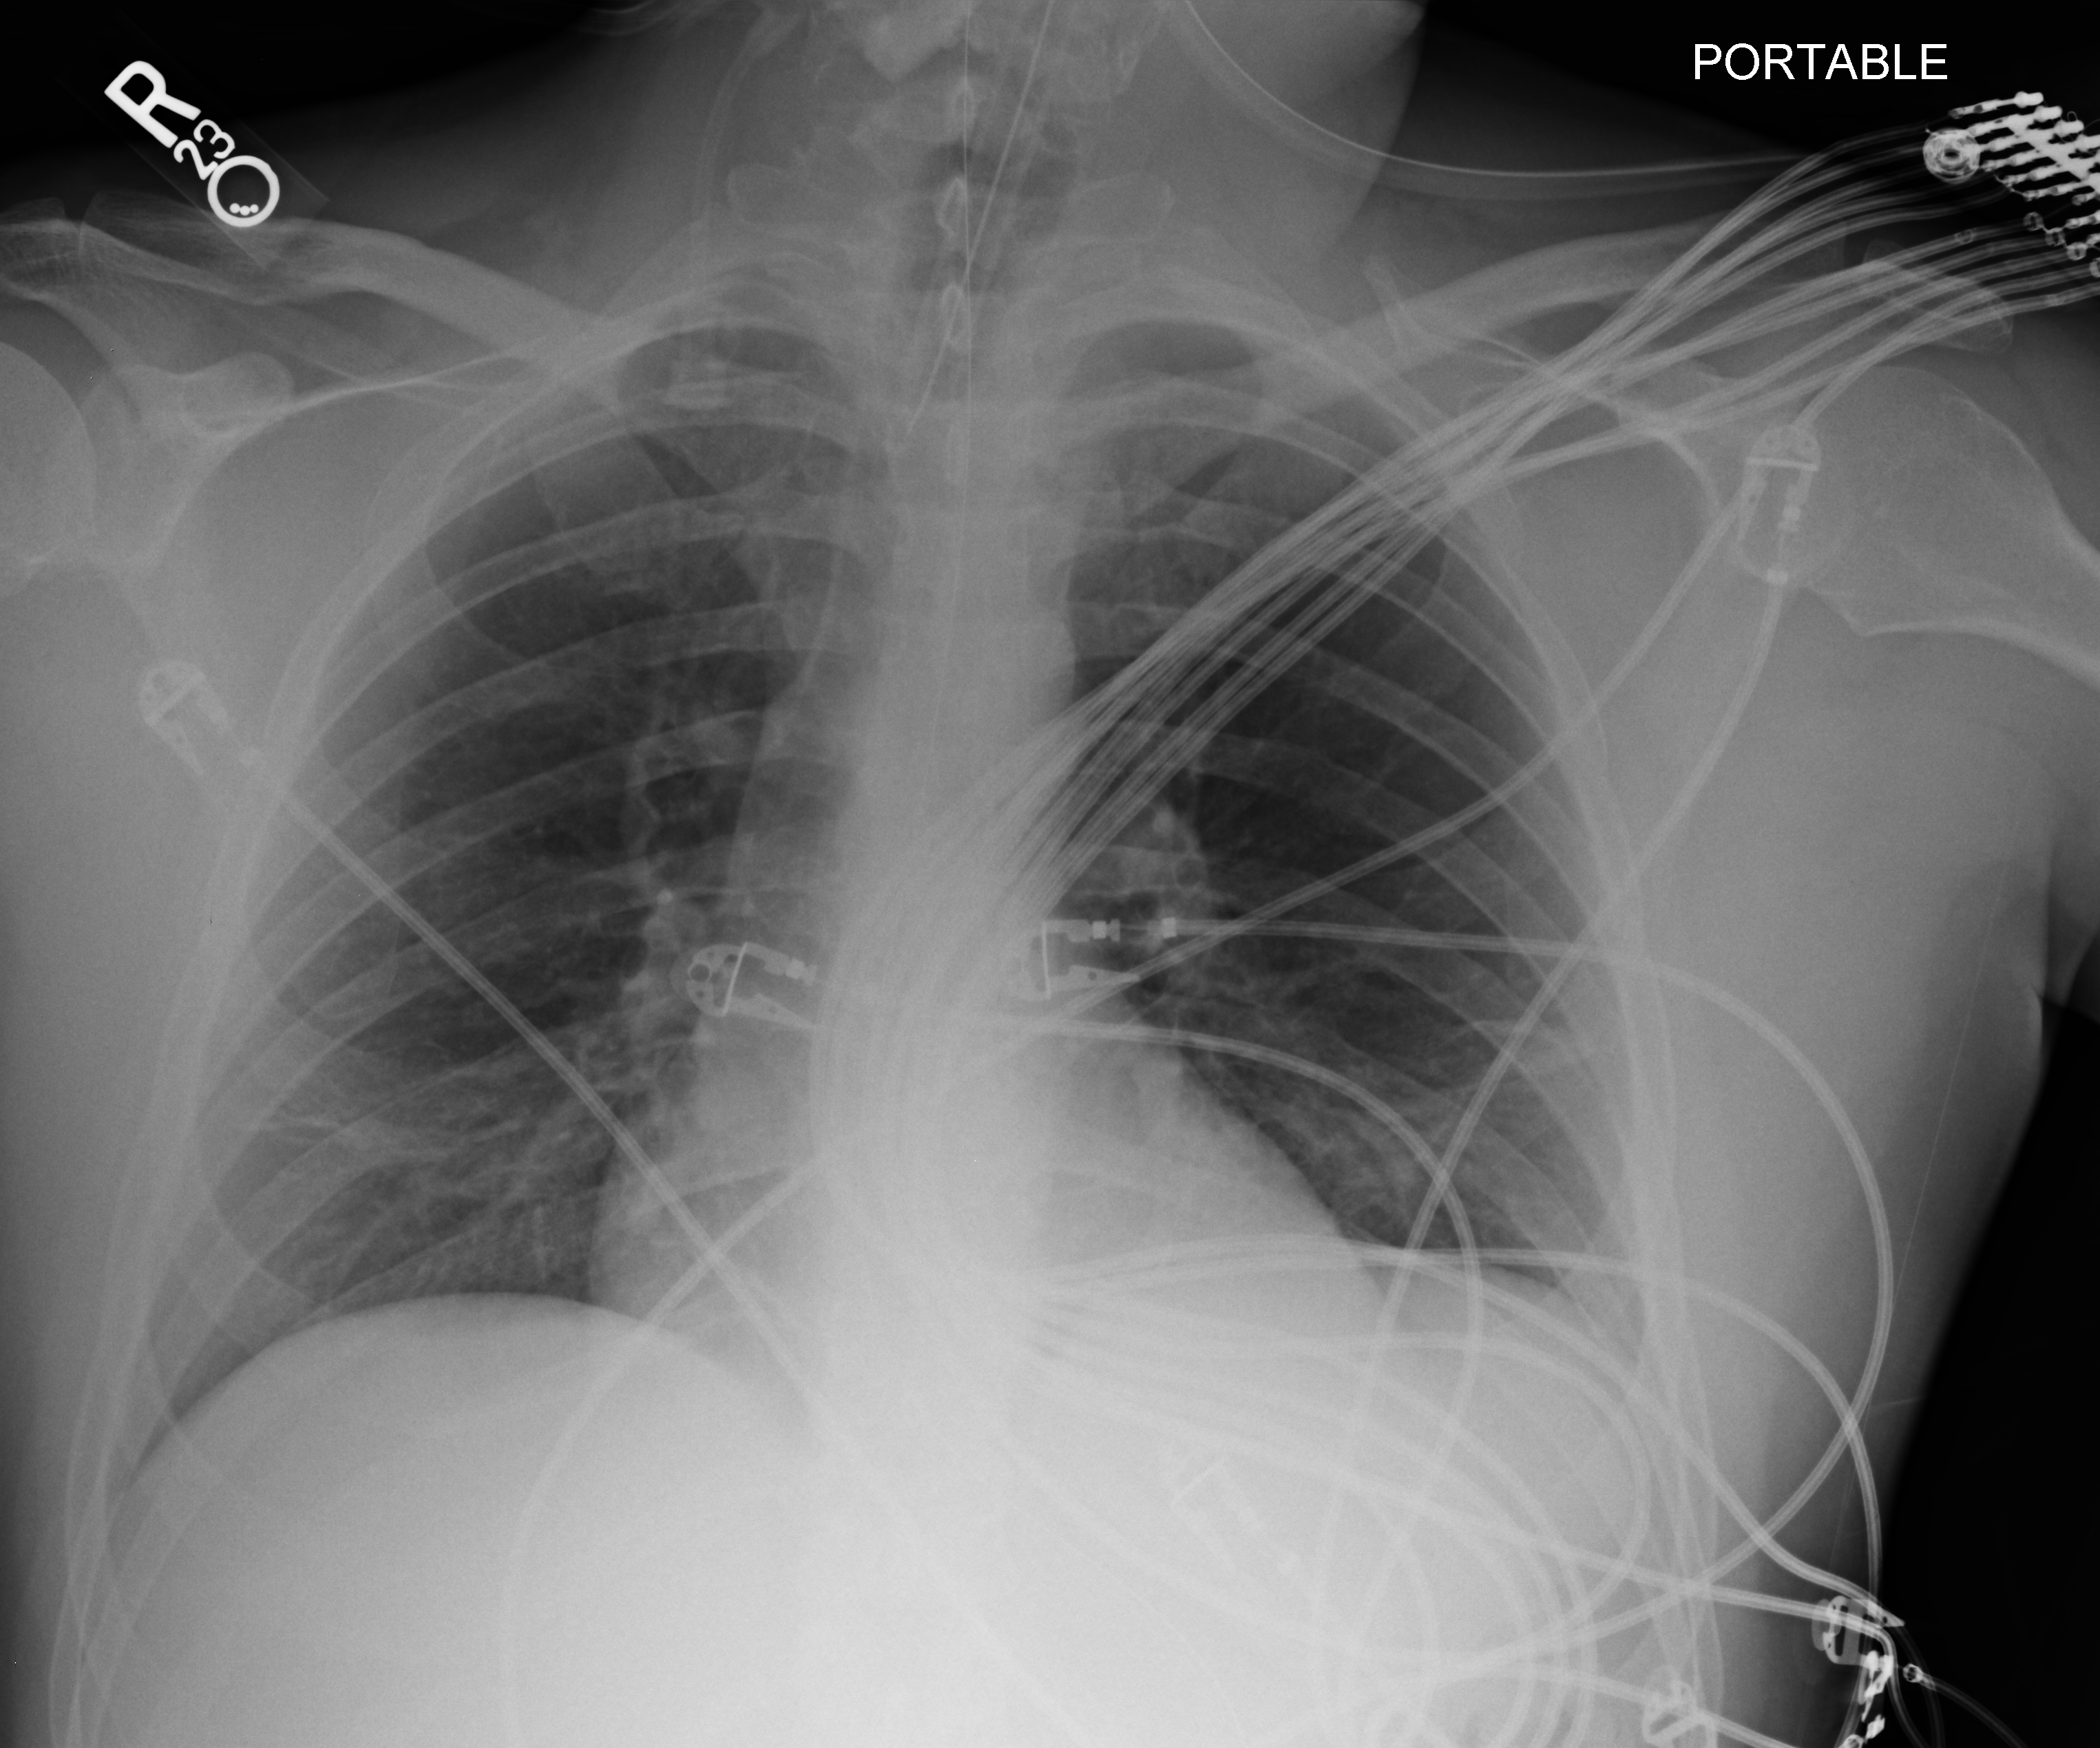
Bedside chest radiograph (computed radiography), anteroposterior (AP) projection. Male patient hospitalised with COVID-19, age 18–59 years.
From the hospital-stay record, not from the radiograph (when in the stay this image was taken is not recorded): mechanically ventilated during this hospital stay: yes.